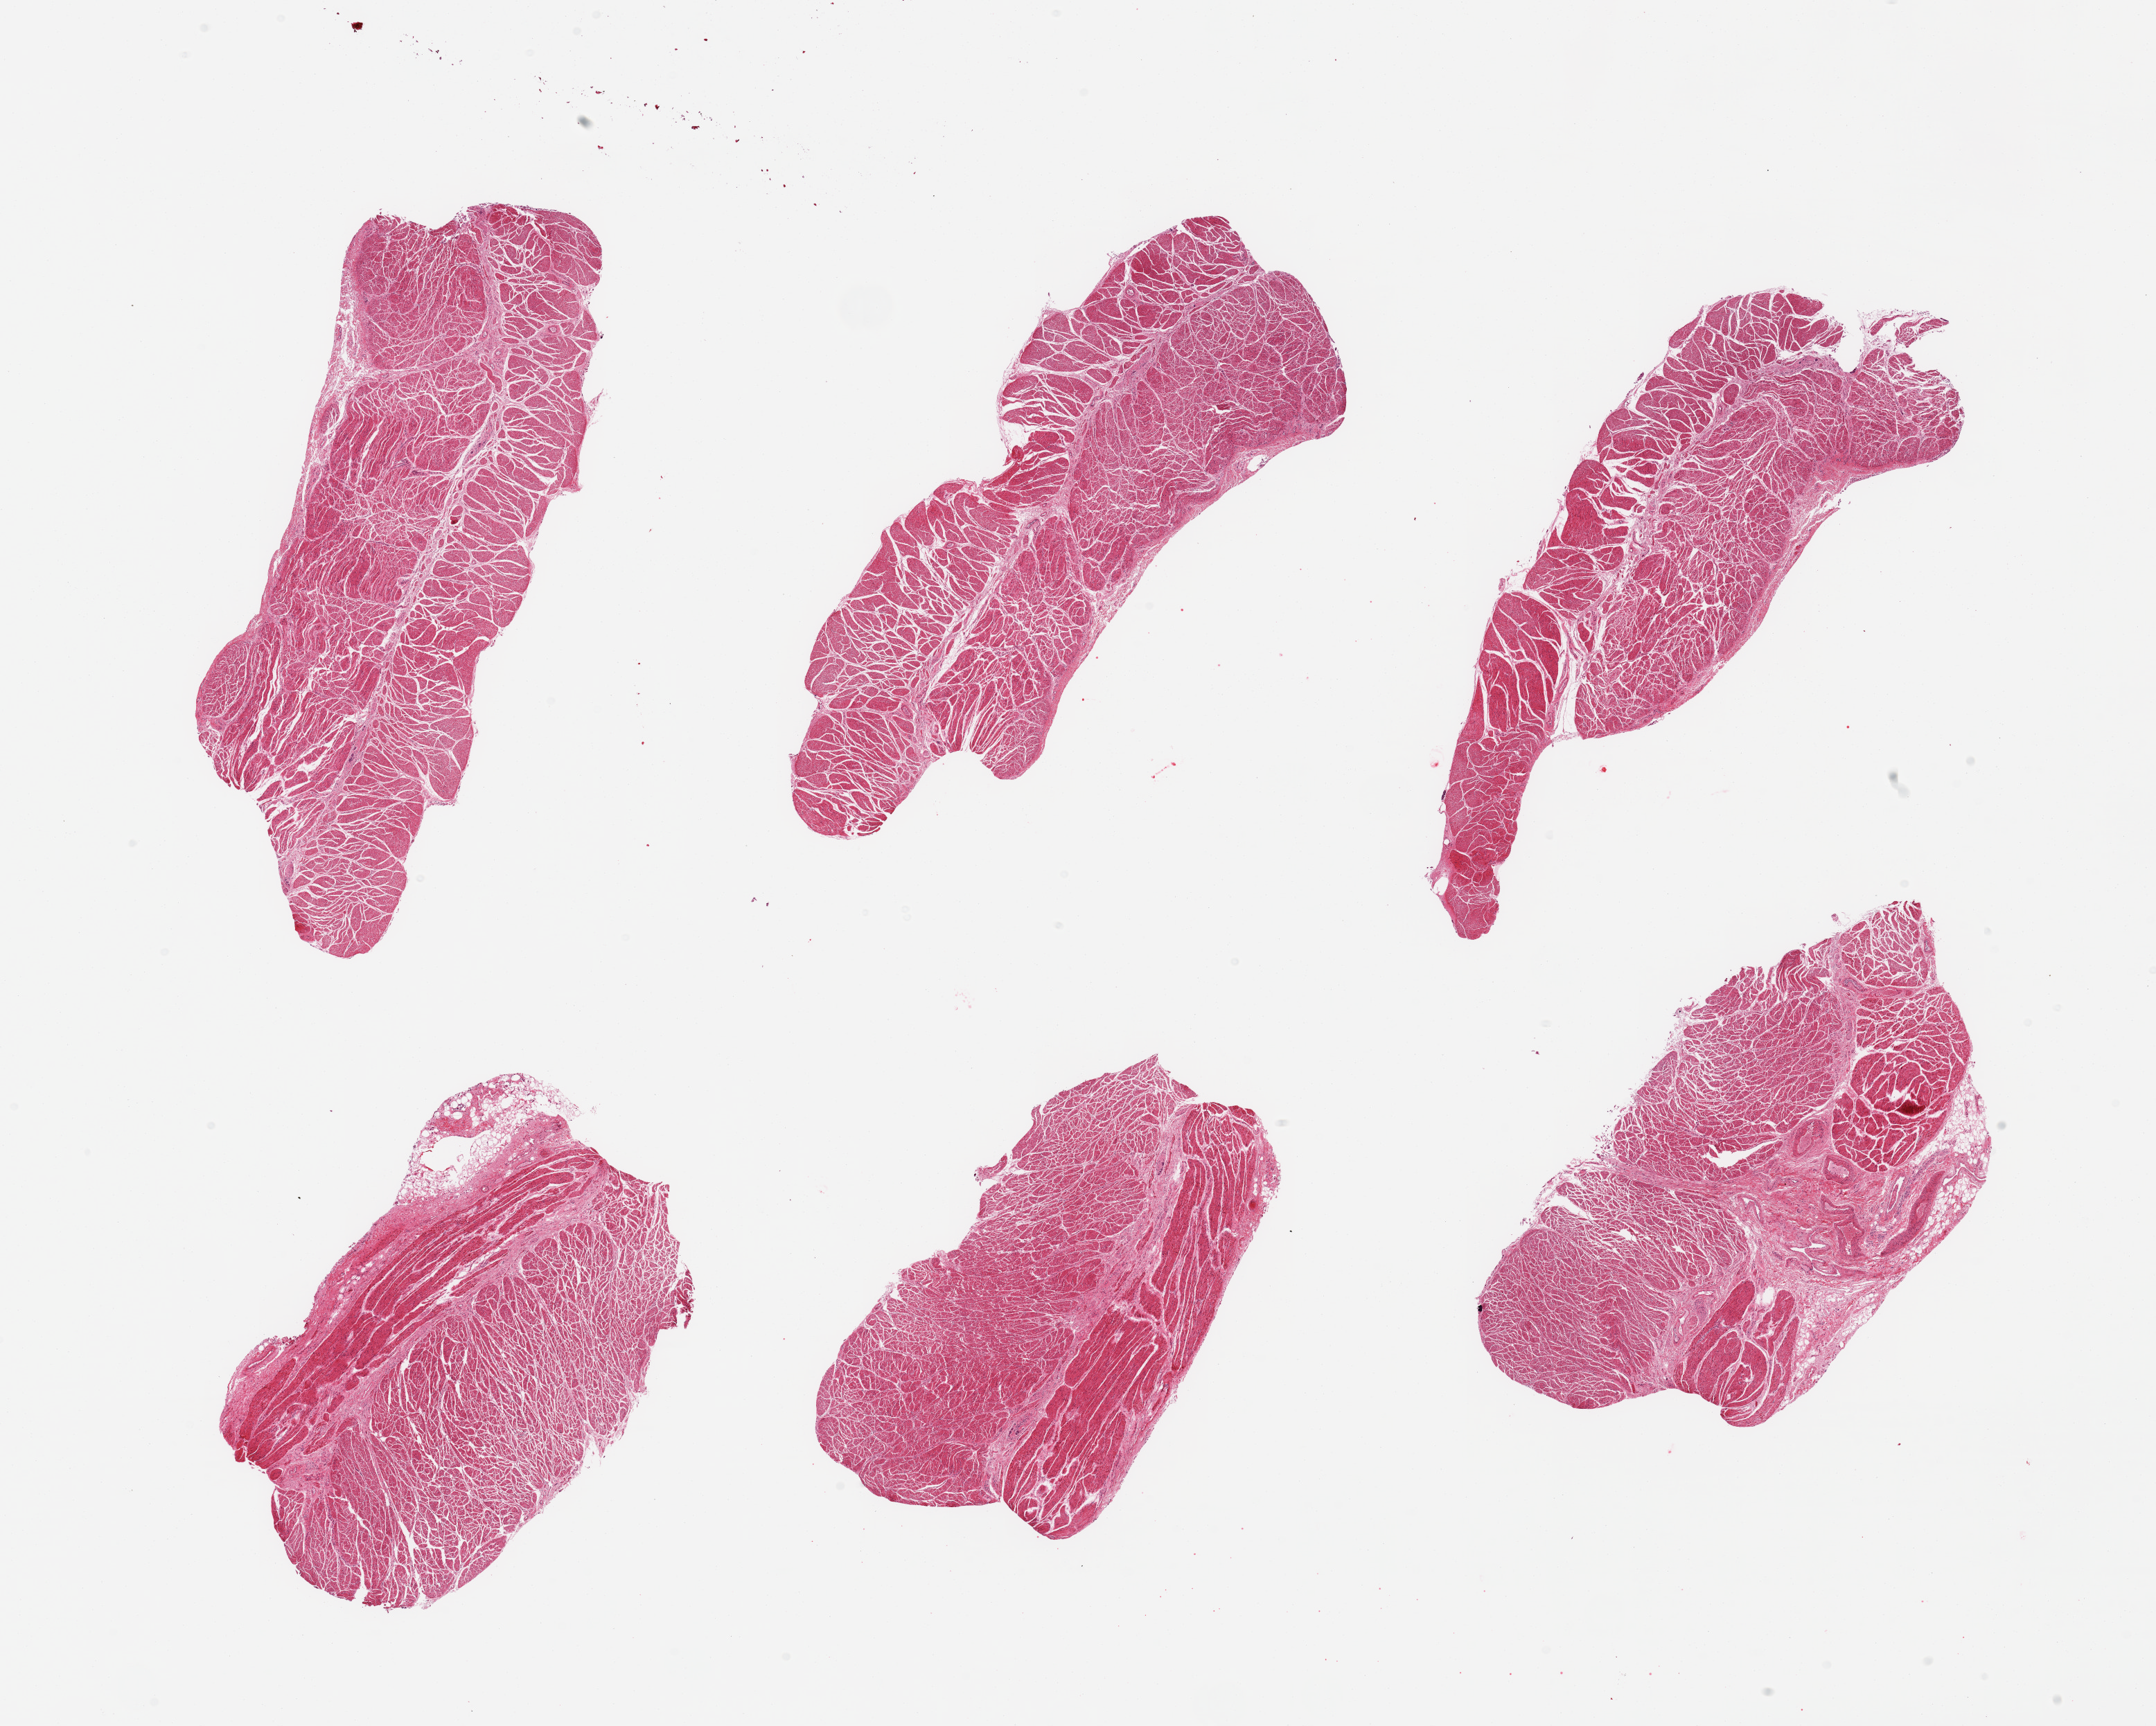
Whole-slide image, hematoxylin and eosin (H&E) stain, brightfield, shown as a low-resolution overview of the whole scanned area (about 24.6 x 19.7 mm), PAXgene-fixed paraffin-embedded (PFPE) section, target tissue: gastroesophageal junction, tissue donor sample. Donor: male.
* reviewer comment on this tissue sample: 6 pieces; well dissected; no artifacts